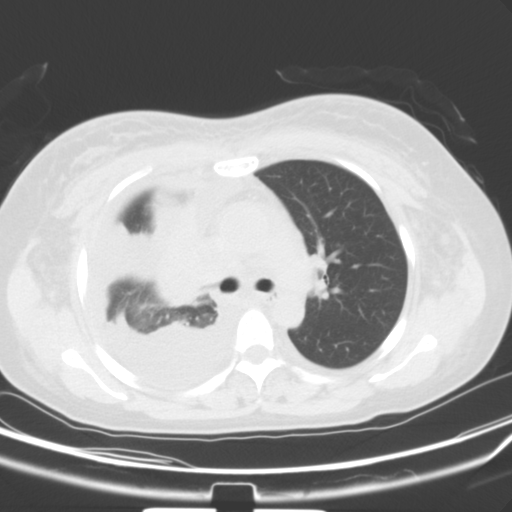
Chest CT, one axial slice; lung window (W 1500 / L -600 HU); 5 mm slice thickness; 512 × 512 image matrix, field of view 347 × 347 mm. Patient: female, 36 years. Case-level facts recorded for this patient, not image findings: clinical TNM (as recorded): T1b N2 M0; histopathological grade: G3.
Structures marked on this image (rectangle marked by the reading radiologist):
- lung tumour (recorded histology: adenocarcinoma): bounding box (x1, y1, x2, y2) in pixels: (151, 206, 215, 307)